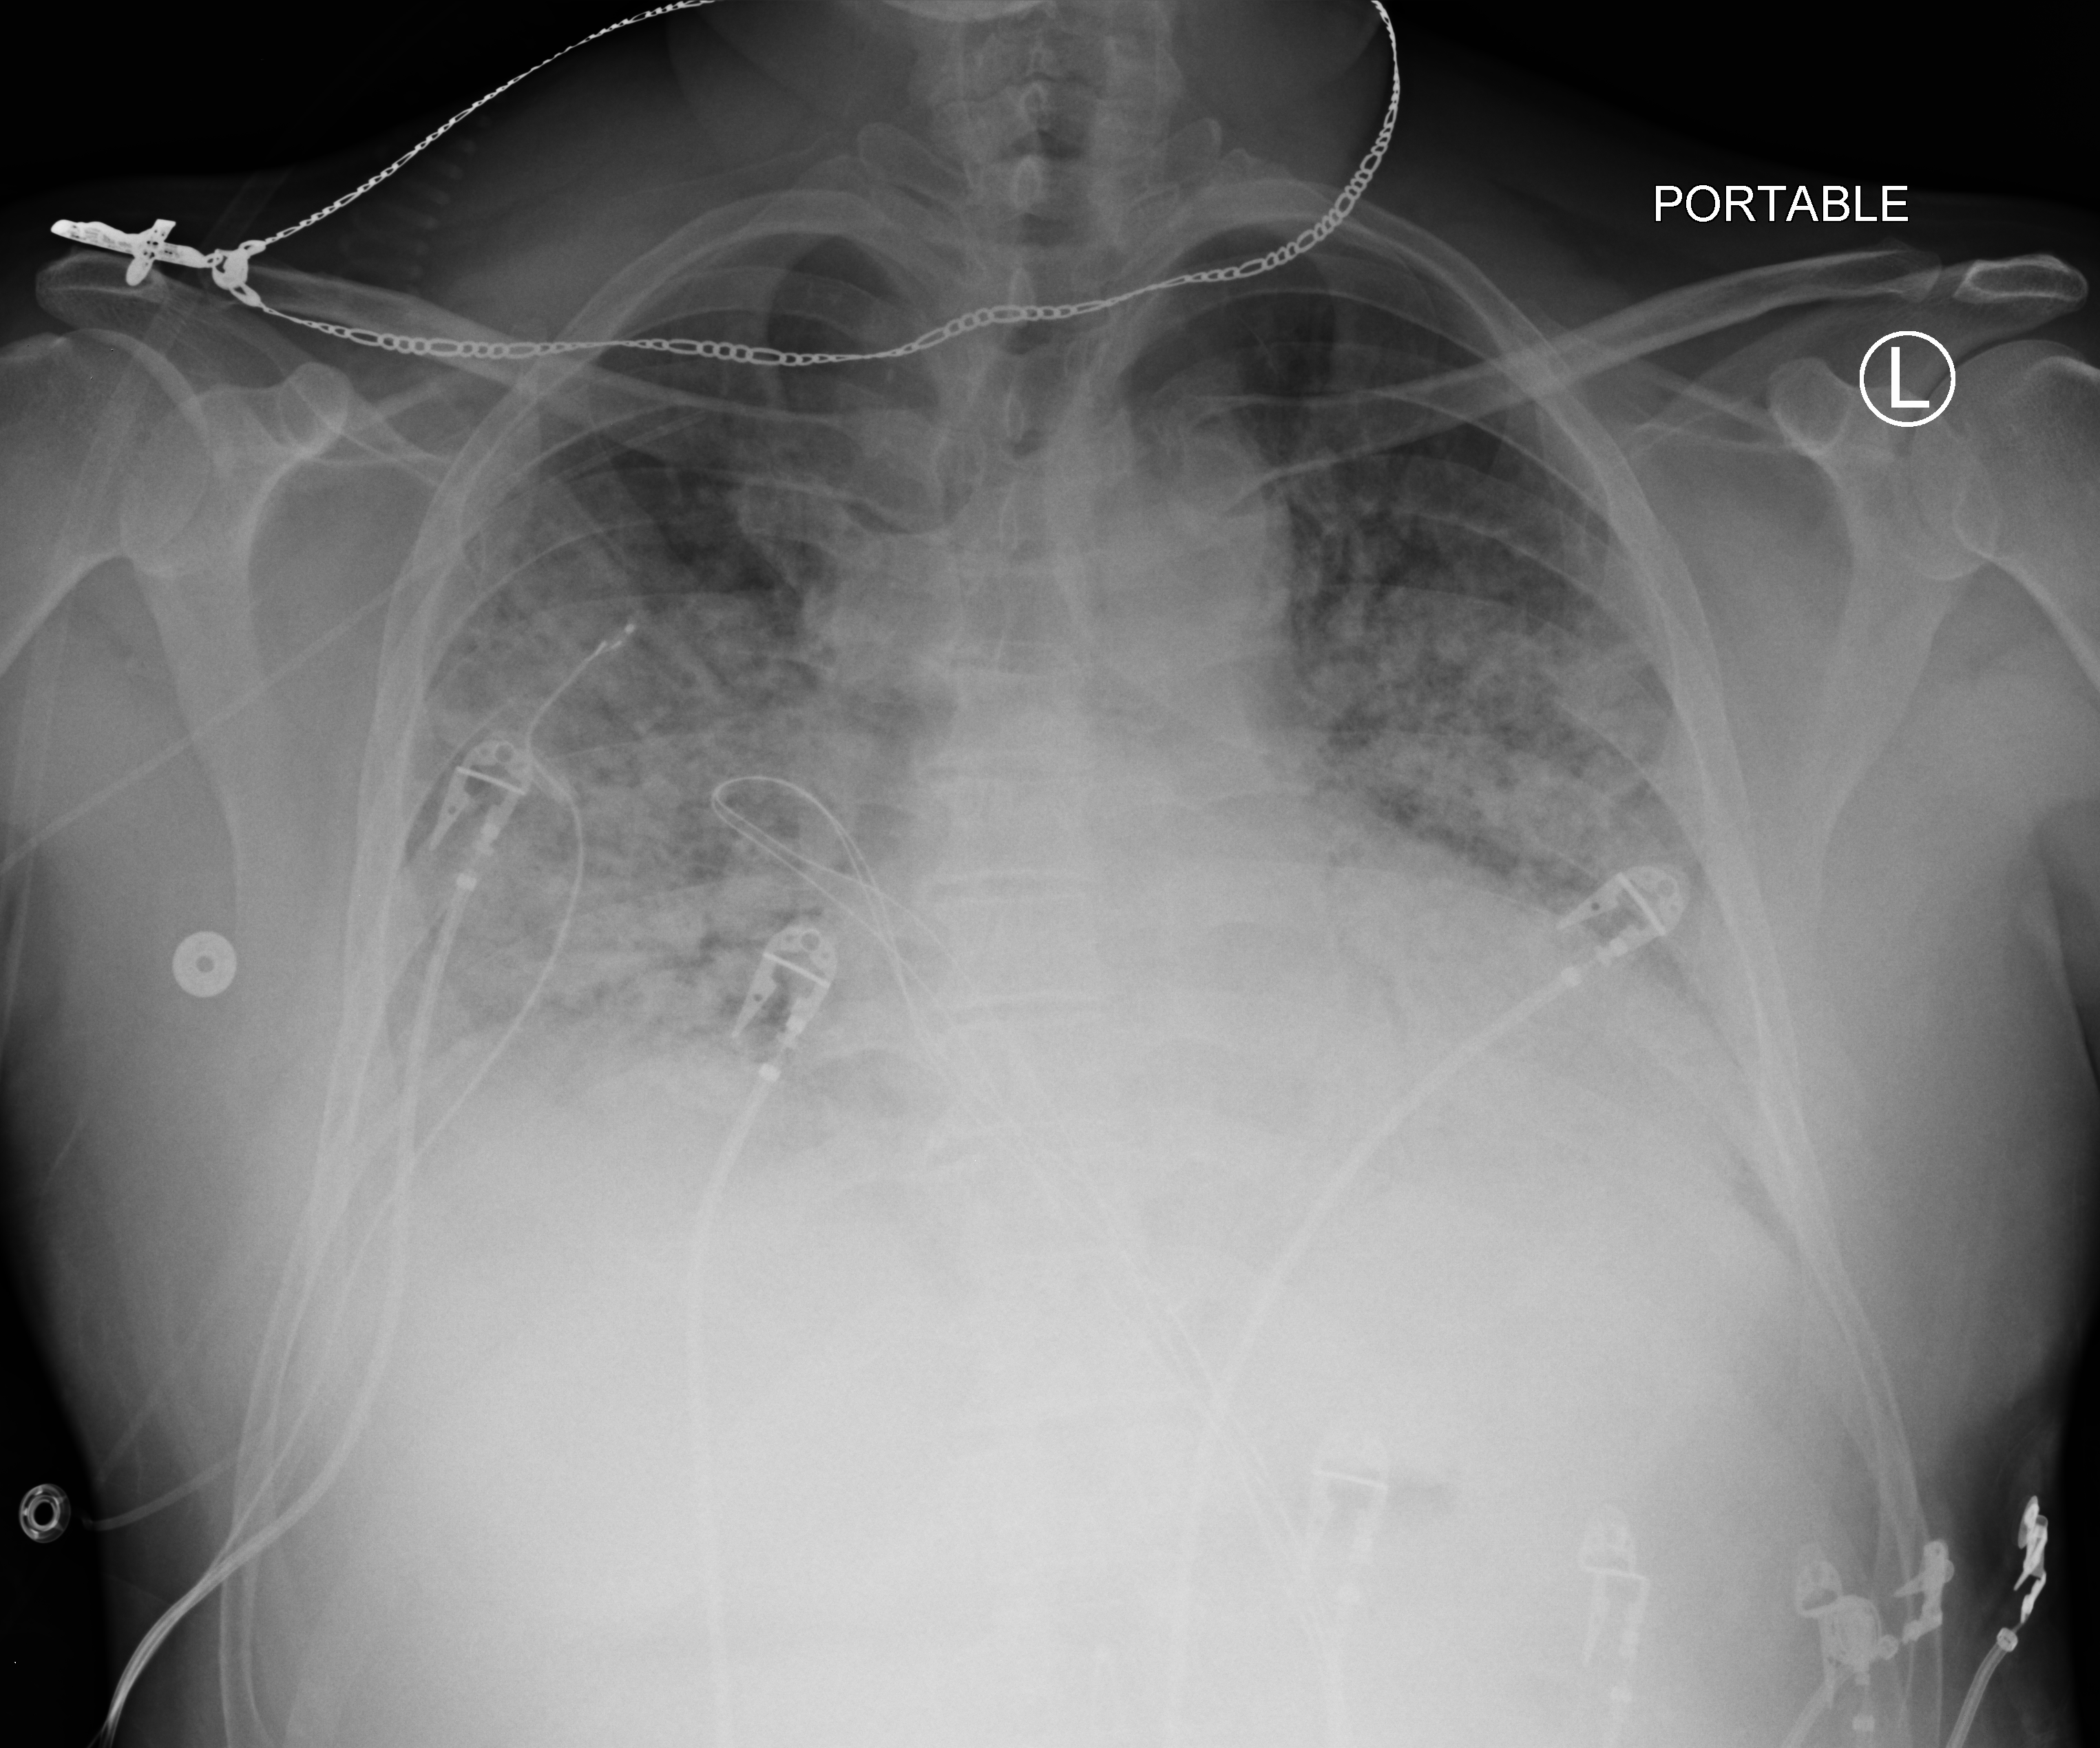
Chest X-ray (portable), anteroposterior (AP) projection. Patient hospitalised with COVID-19; male, aged 18–59 years.
From the hospital-stay record, not from the radiograph (when in the stay this image was taken is not recorded):
- diabetes (admission record): no